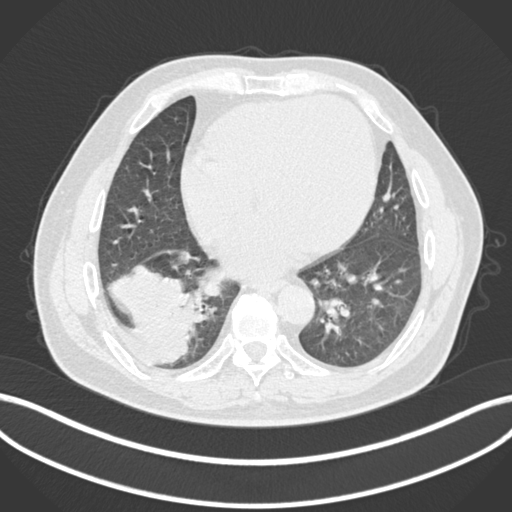
Chest CT, one axial slice. Position 55 of 200 along the scan axis. Reconstruction kernel B30f. 120 kVp. Lung window (W 1500 / L -600 HU). 1 mm slice thickness. 512 × 512 image matrix, field of view 400 × 400 mm. Patient: male, 59 years.
Annotated regions visible in this slice (rectangle marked by the reading radiologist):
- lung tumour (recorded histology: adenocarcinoma): bounding box <104,262,208,367> (left, top, right, bottom; pixels)